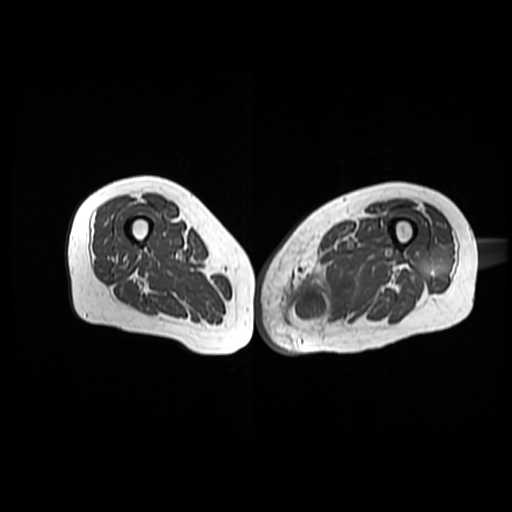
MRI of an extremity soft-tissue mass, one axial slice; position 38 of 42 along the scan axis; 6 mm slice thickness; 512 × 512 image matrix, field of view 420 × 420 mm. Female patient. From the clinical record (not read from this slice): histological type: pleomorphic leiomyosarcoma; grade: high; site of the primary tumour: left thigh.
Structures marked on this image (outlined manually by an expert reader):
- gross tumour volume including surrounding oedema: box from (x=283, y=260) to (x=354, y=330) px